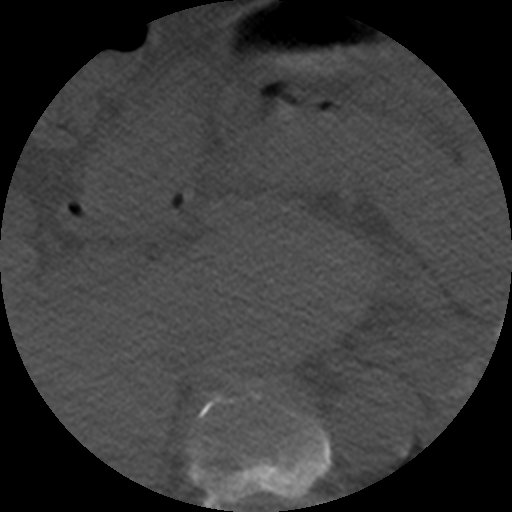
CT including the spine, one axial slice; slice 256 of 508 in the series (ordered by position); 120 kVp; bone window (W 1800 / L 400 HU); 1.25 mm slice thickness; 512 × 512 image matrix, field of view 160 × 160 mm. Patient age 57 years. From the clinical record (not read from this slice): primary cancer: prostate.
Annotated regions visible in this slice (semi-automatic segmentation, software-assisted and operator-edited):
- T10 vertebra: bounding box (x1, y1, x2, y2) in pixels: (189, 382, 331, 509)